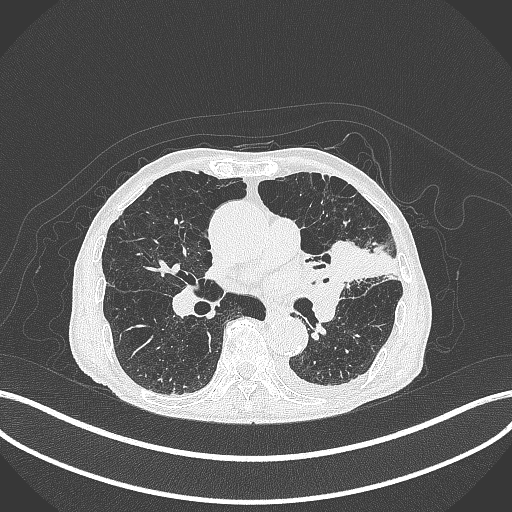
Chest CT, one axial slice. Slice 201 of 385 in the series (ordered by position). Lung window (W 1500 / L -600 HU). 512 × 512 image matrix, field of view 400 × 400 mm. Male patient, age 90 years or older. From the clinical record (not read from this slice): clinical TNM (as recorded): T2b N1 M0.
Structures marked on this image (bounding box drawn by a radiologist):
- lung tumour (recorded histology: squamous cell carcinoma): bounding box <321,232,380,293> (left, top, right, bottom; pixels)